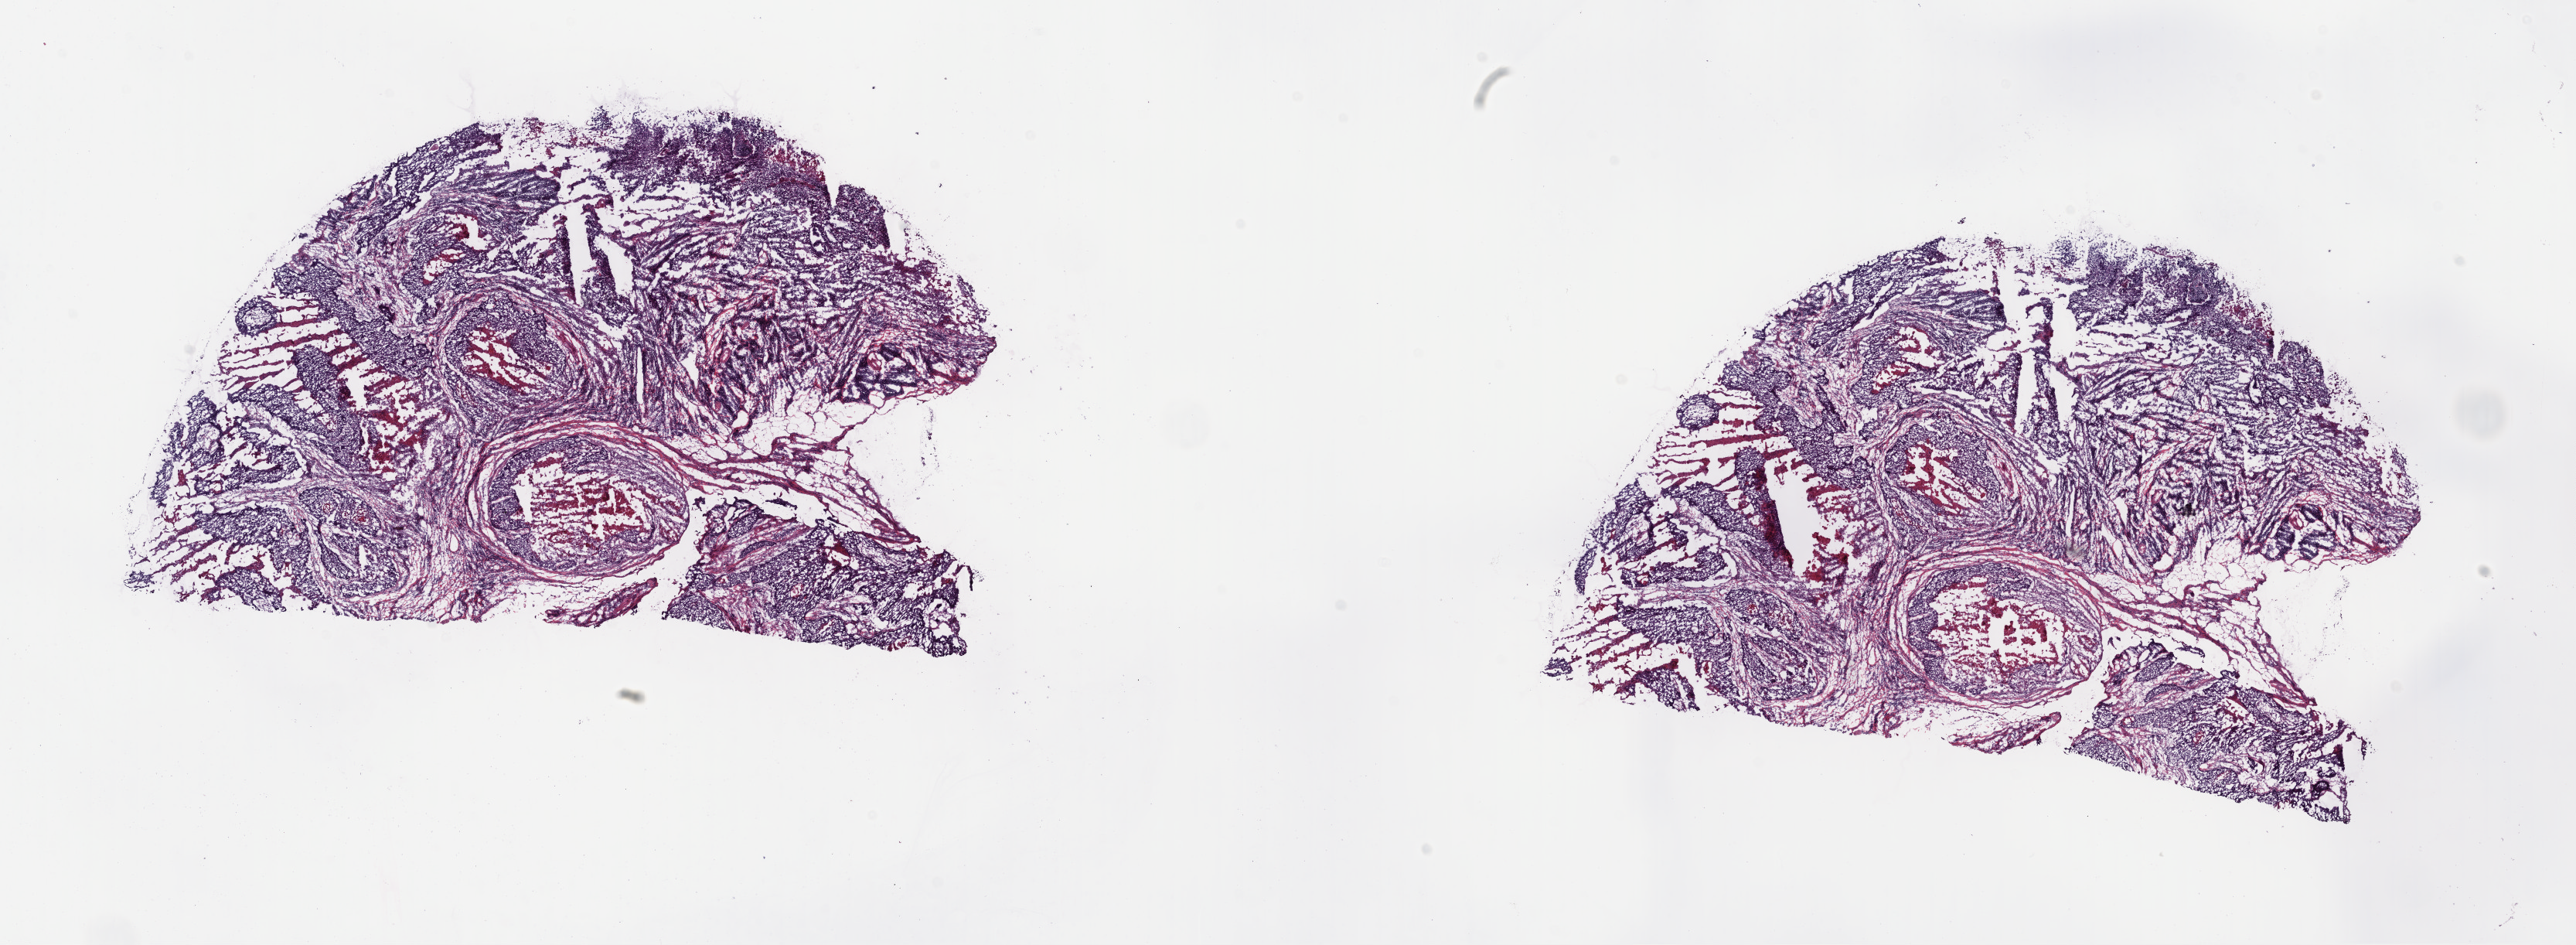
H&E-stained whole-slide image — a low-resolution overview of the entire scanned area, about 26.2 x 9.6 mm (from a 40x scan), frozen section, sample: primary tumour, head and neck. Patient: male, age at initial diagnosis 75 years. Histologic grade: G2 (moderately differentiated). Composition of this section per pathologist review: tumour cells 65%, tumour nuclei 80%, normal cells 0%, stromal cells 25%, necrosis 10%. Infiltration values recorded for this section: lymphocyte infiltration 0%, monocyte infiltration 0%, neutrophil infiltration 0%.
- AJCC pathologic stage: II
- TNM: T2 N0 M0
- lymph nodes positive (case pathology): 0 of 48 examined
- diagnosis: Squamous cell carcinoma, NOS (larynx, NOS)